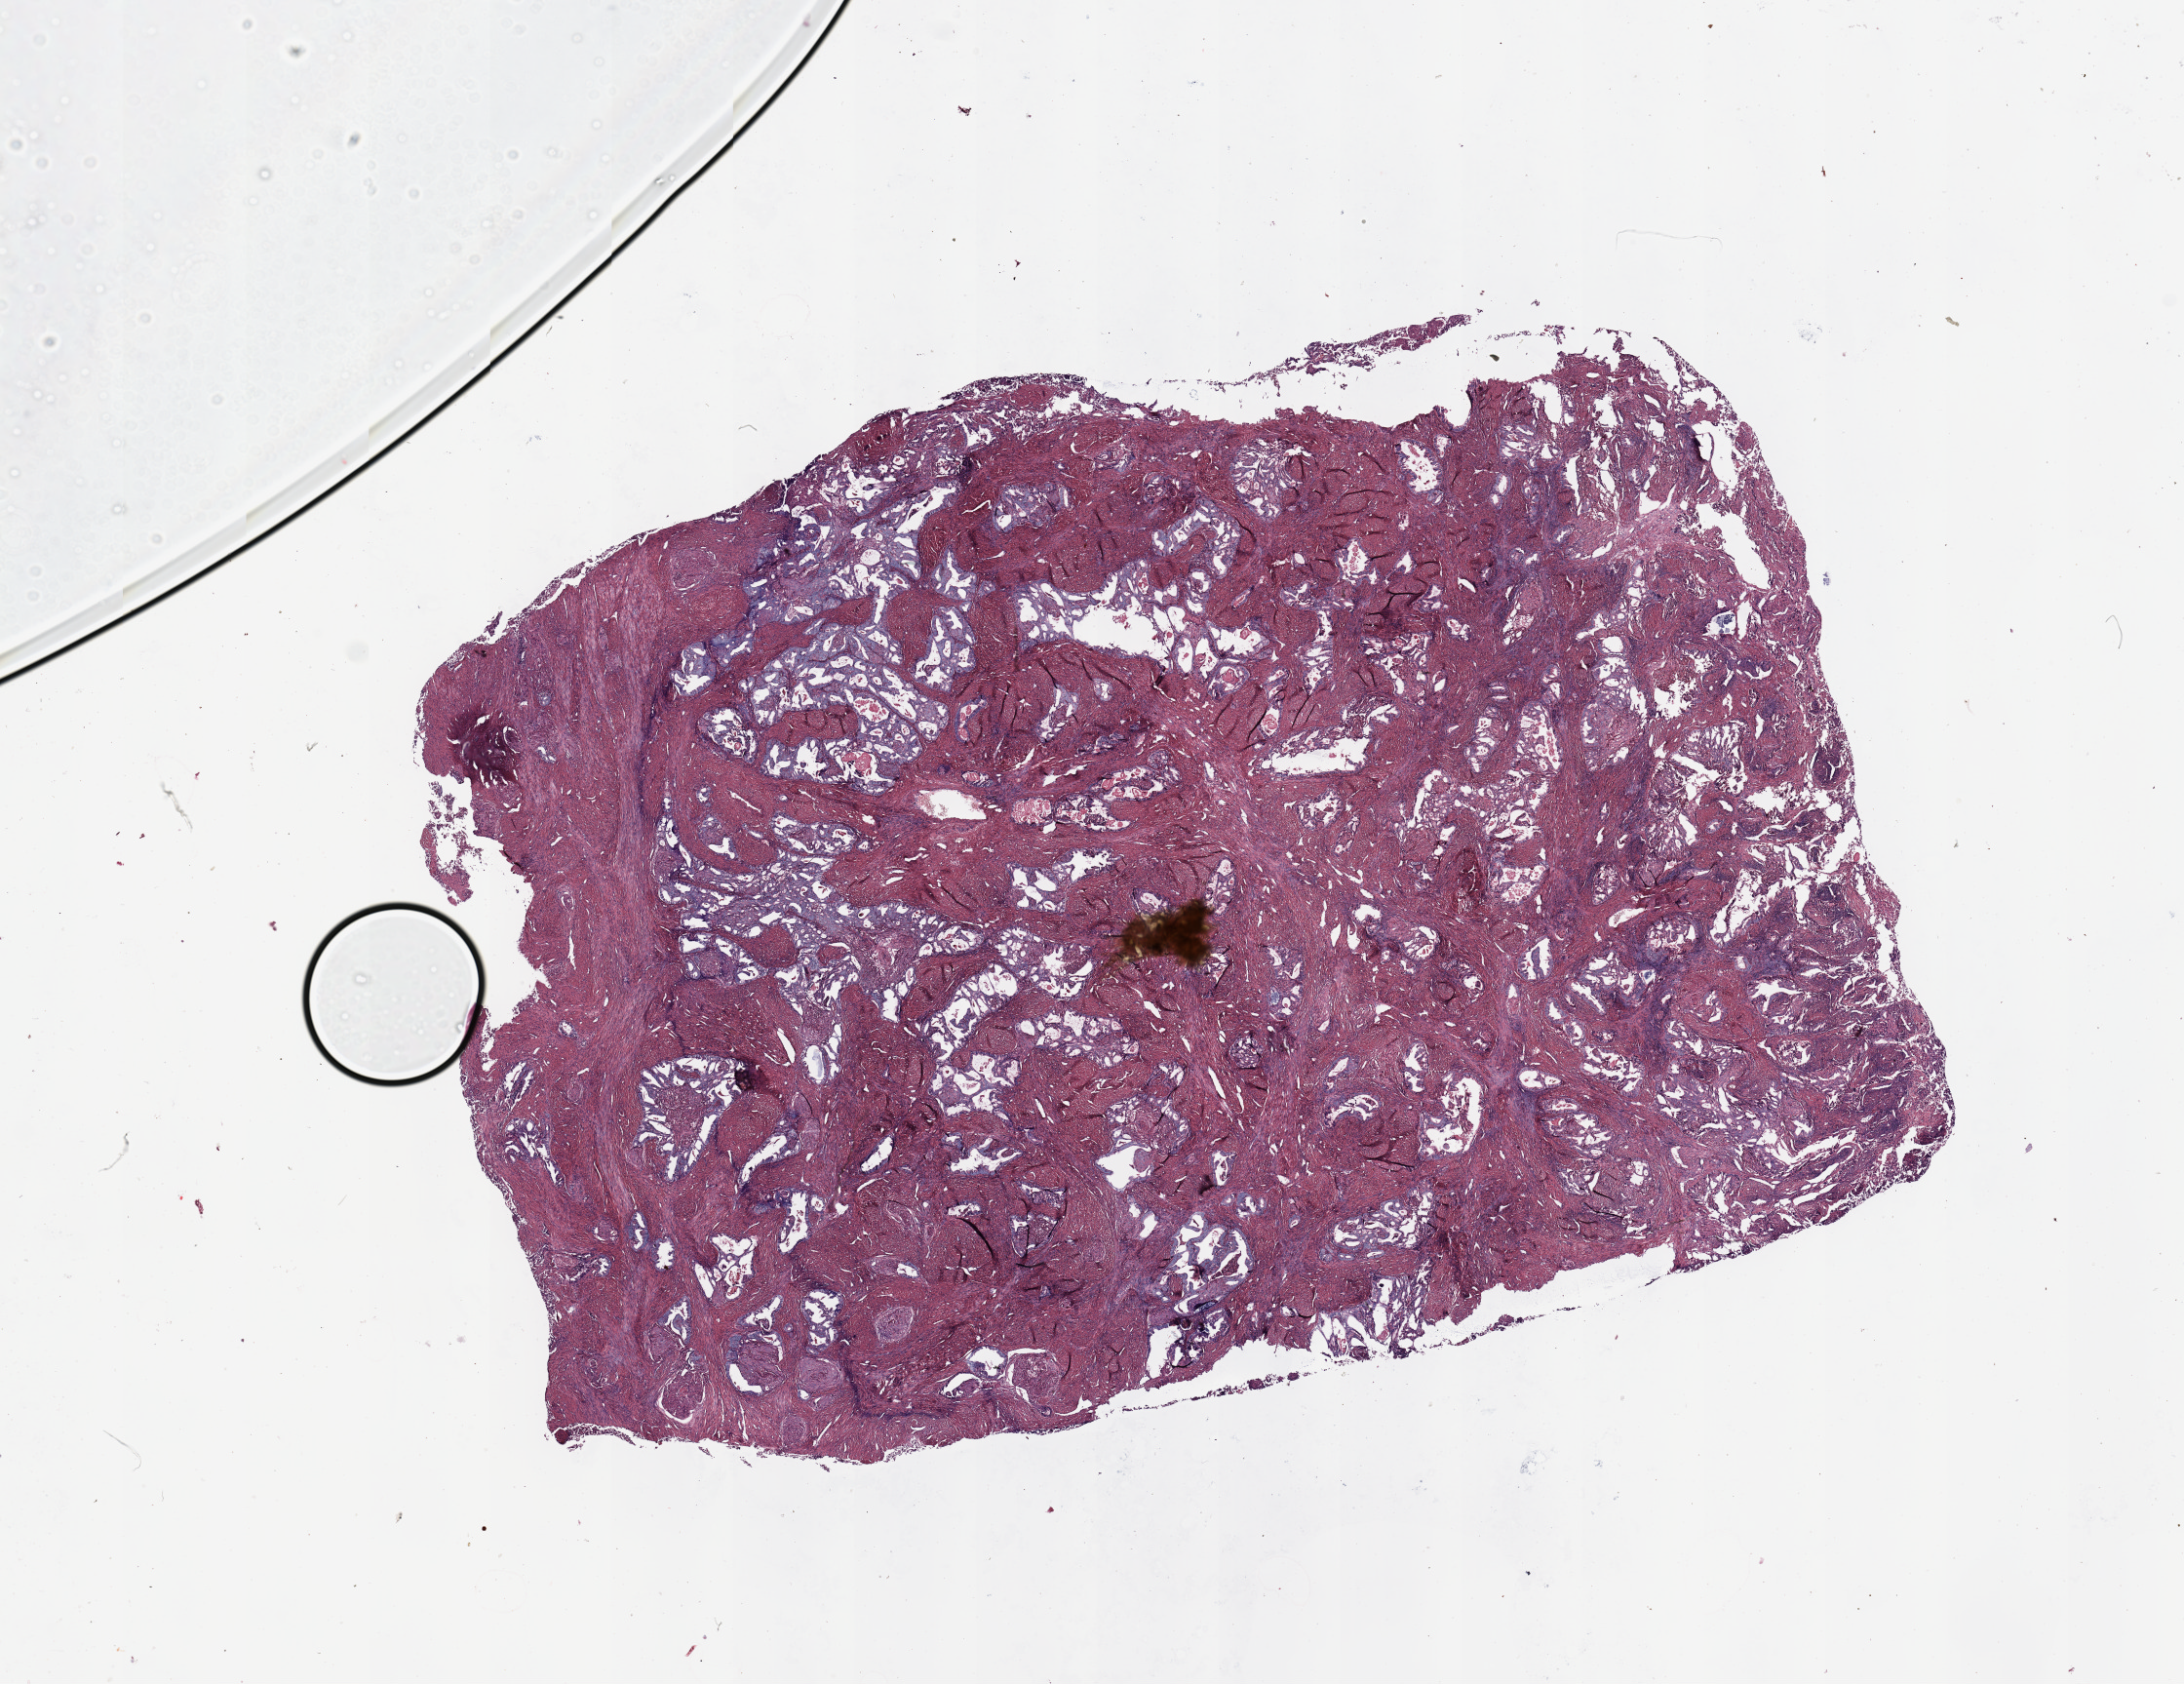
Whole-slide histology image, Hematoxylin and eosin (H&E) stained — whole scanned area (about 17.7 x 13.7 mm, slide scanned at 20x) shown as a low-resolution overview; tumour tissue sample, uterus. Patient: female, age 57 years. Histologic grade: G2 (moderately differentiated).
* AJCC pathologic stage: III
* diagnosis: Endometrioid adenocarcinoma, NOS